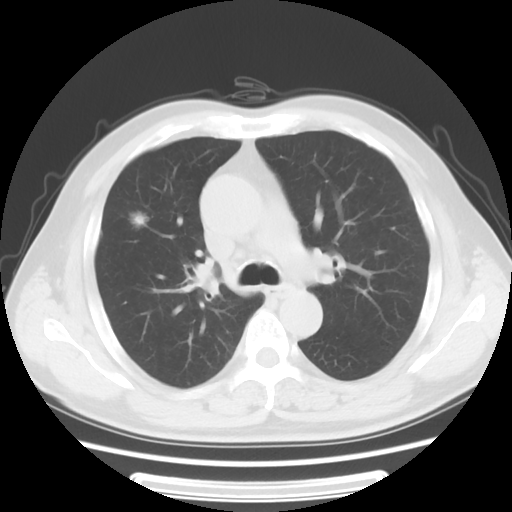
Chest CT, one axial slice. Slice 39 of 63 in the series (ordered by position). Reconstruction kernel STANDARD. 120 kVp. Lung window (W 1500 / L -600 HU). 5 mm slice thickness. 512 × 512 image matrix. Male patient, age 63 years. From the clinical record (not read from this slice): clinical TNM (as recorded): T1c N0 M0; histopathological grade: G2-3.
Annotated regions visible in this slice (bounding box drawn by a radiologist):
- lung tumour (recorded histology: adenocarcinoma): box from (x=124, y=206) to (x=169, y=248) px